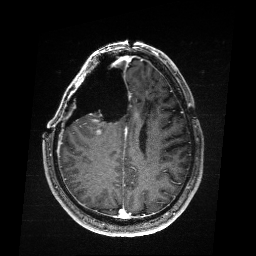
Brain MRI from a brain-tumour surgery series, one axial slice; slice 72 of 176 in the series (ordered by position); T1-weighted post-contrast; 256 × 256 image matrix, field of view 256 × 256 mm. Case-level facts recorded for this patient, not image findings: histopathology: Astrocytoma; WHO grade: 4; IDH mutation: yes; tumour location: Right Frontal.
Structures marked on this image (expert manual segmentation):
- residual tumour: box from (x=97, y=118) to (x=105, y=135) px